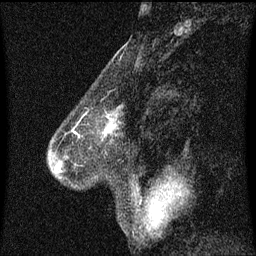
Breast MRI (dynamic contrast-enhanced), one sagittal slice. Slice 28 of 60 in the series (ordered by position). Dynamic contrast-enhanced series, image 2 of 3 at this slice position (ordered by acquisition). 1.5 T. TE 4.2 ms, TR 8.4 ms. 2 mm slice thickness. 256 × 256 image matrix. Female patient, age 58 years.
Annotated regions visible in this slice (semi-automatic segmentation, software-assisted and operator-edited):
- analysis volume of interest (the breast-tissue region the enhancement analysis was run in; not a lesion): bounding box <79,106,123,143> (left, top, right, bottom; pixels)
- tumour enhancement mask (voxels above the 70 % enhancement threshold inside the analysis volume of interest): <105,122,114,135>